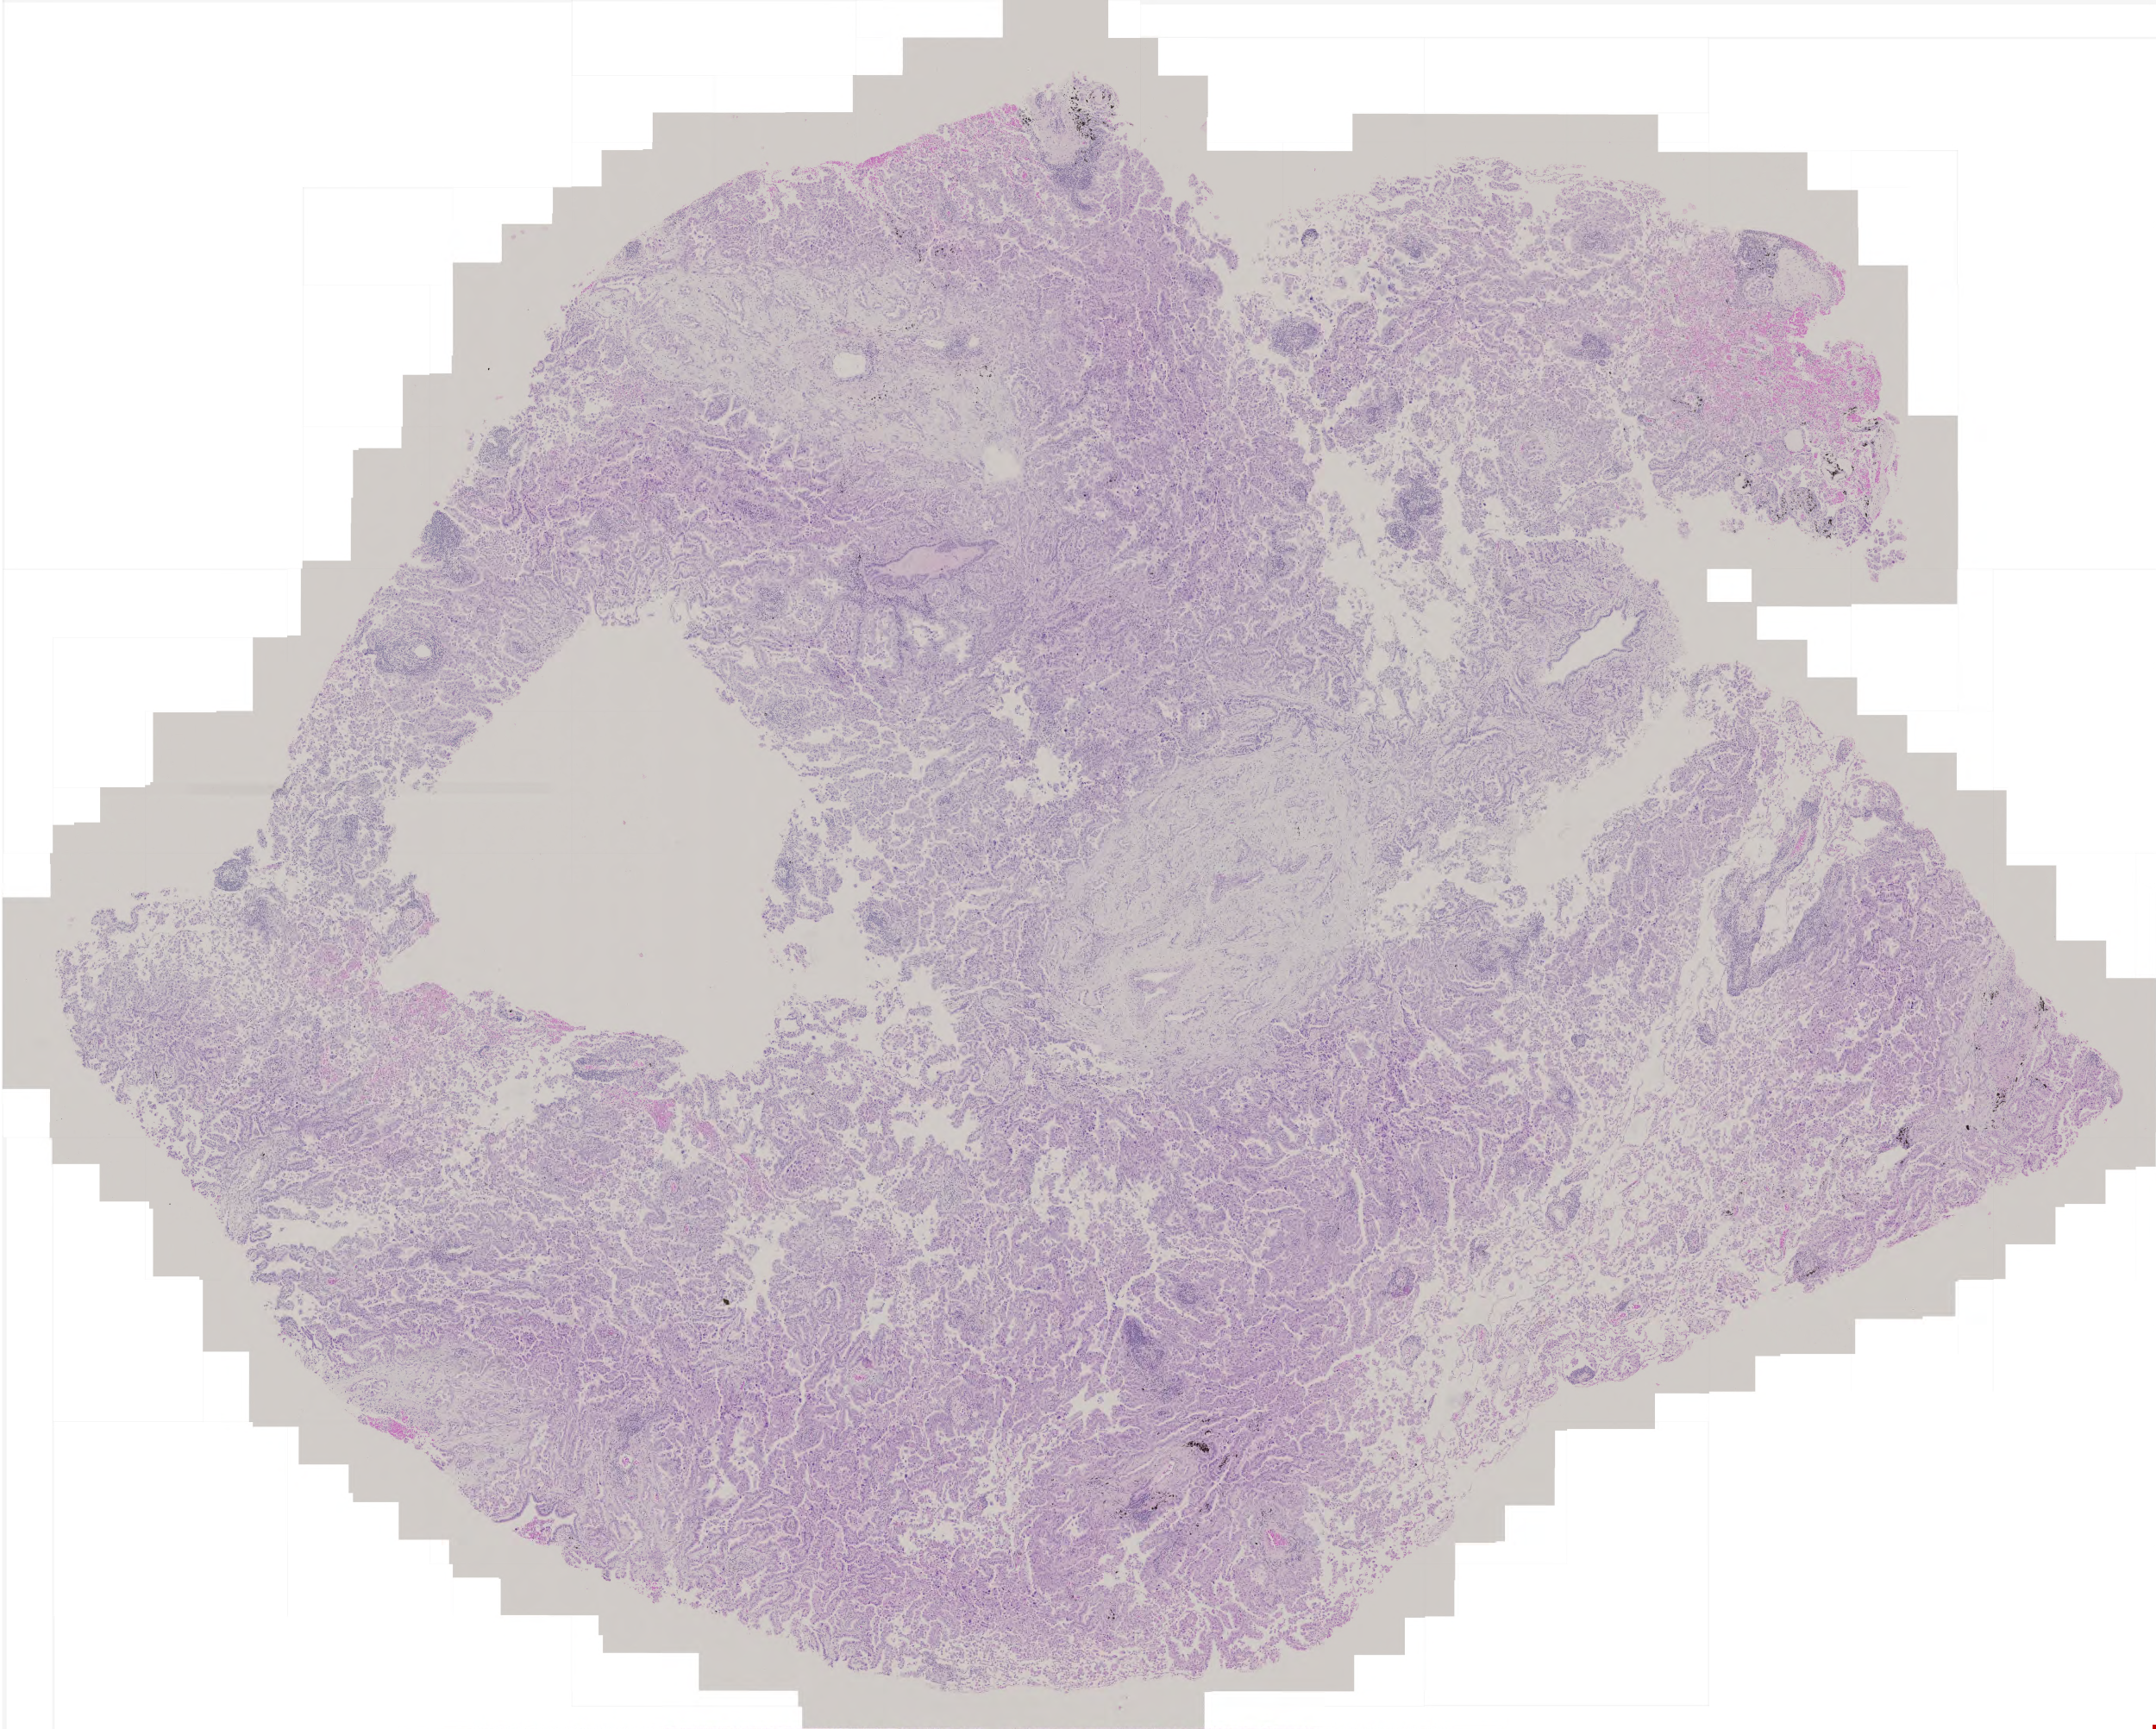
Whole-slide histology image, Hematoxylin and eosin (H&E) stained, low-resolution overview of the scanned area, about 5.0 x 4.0 mm, formalin-fixed paraffin-embedded (FFPE) diagnostic section, lung, primary tumour sample. Male patient; age at initial diagnosis 65 years.
Laterality: left. Diagnosis: Adenocarcinoma with mixed subtypes. AJCC pathologic stage: IIB (6th edition).